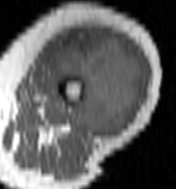
MRI of an extremity soft-tissue mass, one axial slice. Slice 48 of 100 in the series (ordered by position). MR volume resampled by the dataset authors to the PET/CT grid (not the native acquisition matrix). 3.27 mm slice thickness. 176 × 189 image matrix. Female patient. From the clinical record (not read from this slice): histological type: undifferentiated – high grade; grade: high; site of the primary tumour: left thigh.
Structures marked on this image (expert contour drawn on MRI and transferred to this co-registered scan by the dataset authors):
- gross tumour volume including surrounding oedema: bounding box [x1, y1, x2, y2] px = [53, 32, 143, 138]
- gross tumour volume (mass): [55, 32, 143, 138]